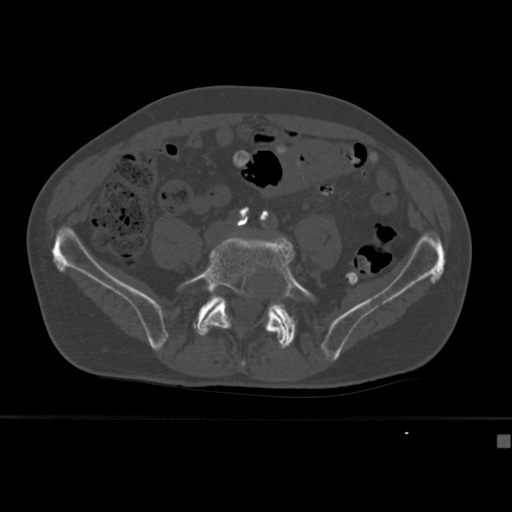
CT including the spine, one axial slice. Position 85 of 430 along the scan axis. Reconstruction kernel Br40s. 120 kVp. Bone window (W 1800 / L 400 HU). 1.5 mm slice thickness. 512 × 512 image matrix. Male patient, age 64 years. From the clinical record (not read from this slice): primary cancer: uterus.
Outlined on this slice (semi-automatically segmented with operator editing):
- L5 vertebra: bounding box <178,235,317,349> (left, top, right, bottom; pixels)